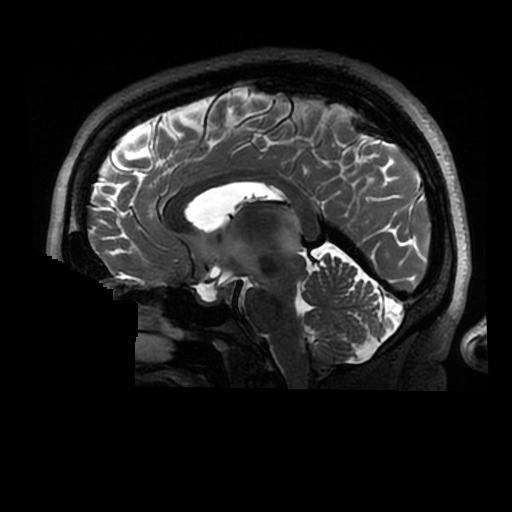
Brain MRI from a brain-tumour surgery series, one sagittal slice; position 155 of 320 along the scan axis; 0.6 mm slice thickness; 512 × 512 image matrix. Case-level facts recorded for this patient, not image findings: histopathology: Astrocytoma; WHO grade: 2; IDH mutation: yes.
Annotated regions visible in this slice (outlined manually by an expert reader):
- tumour: box from (x=276, y=209) to (x=301, y=257) px